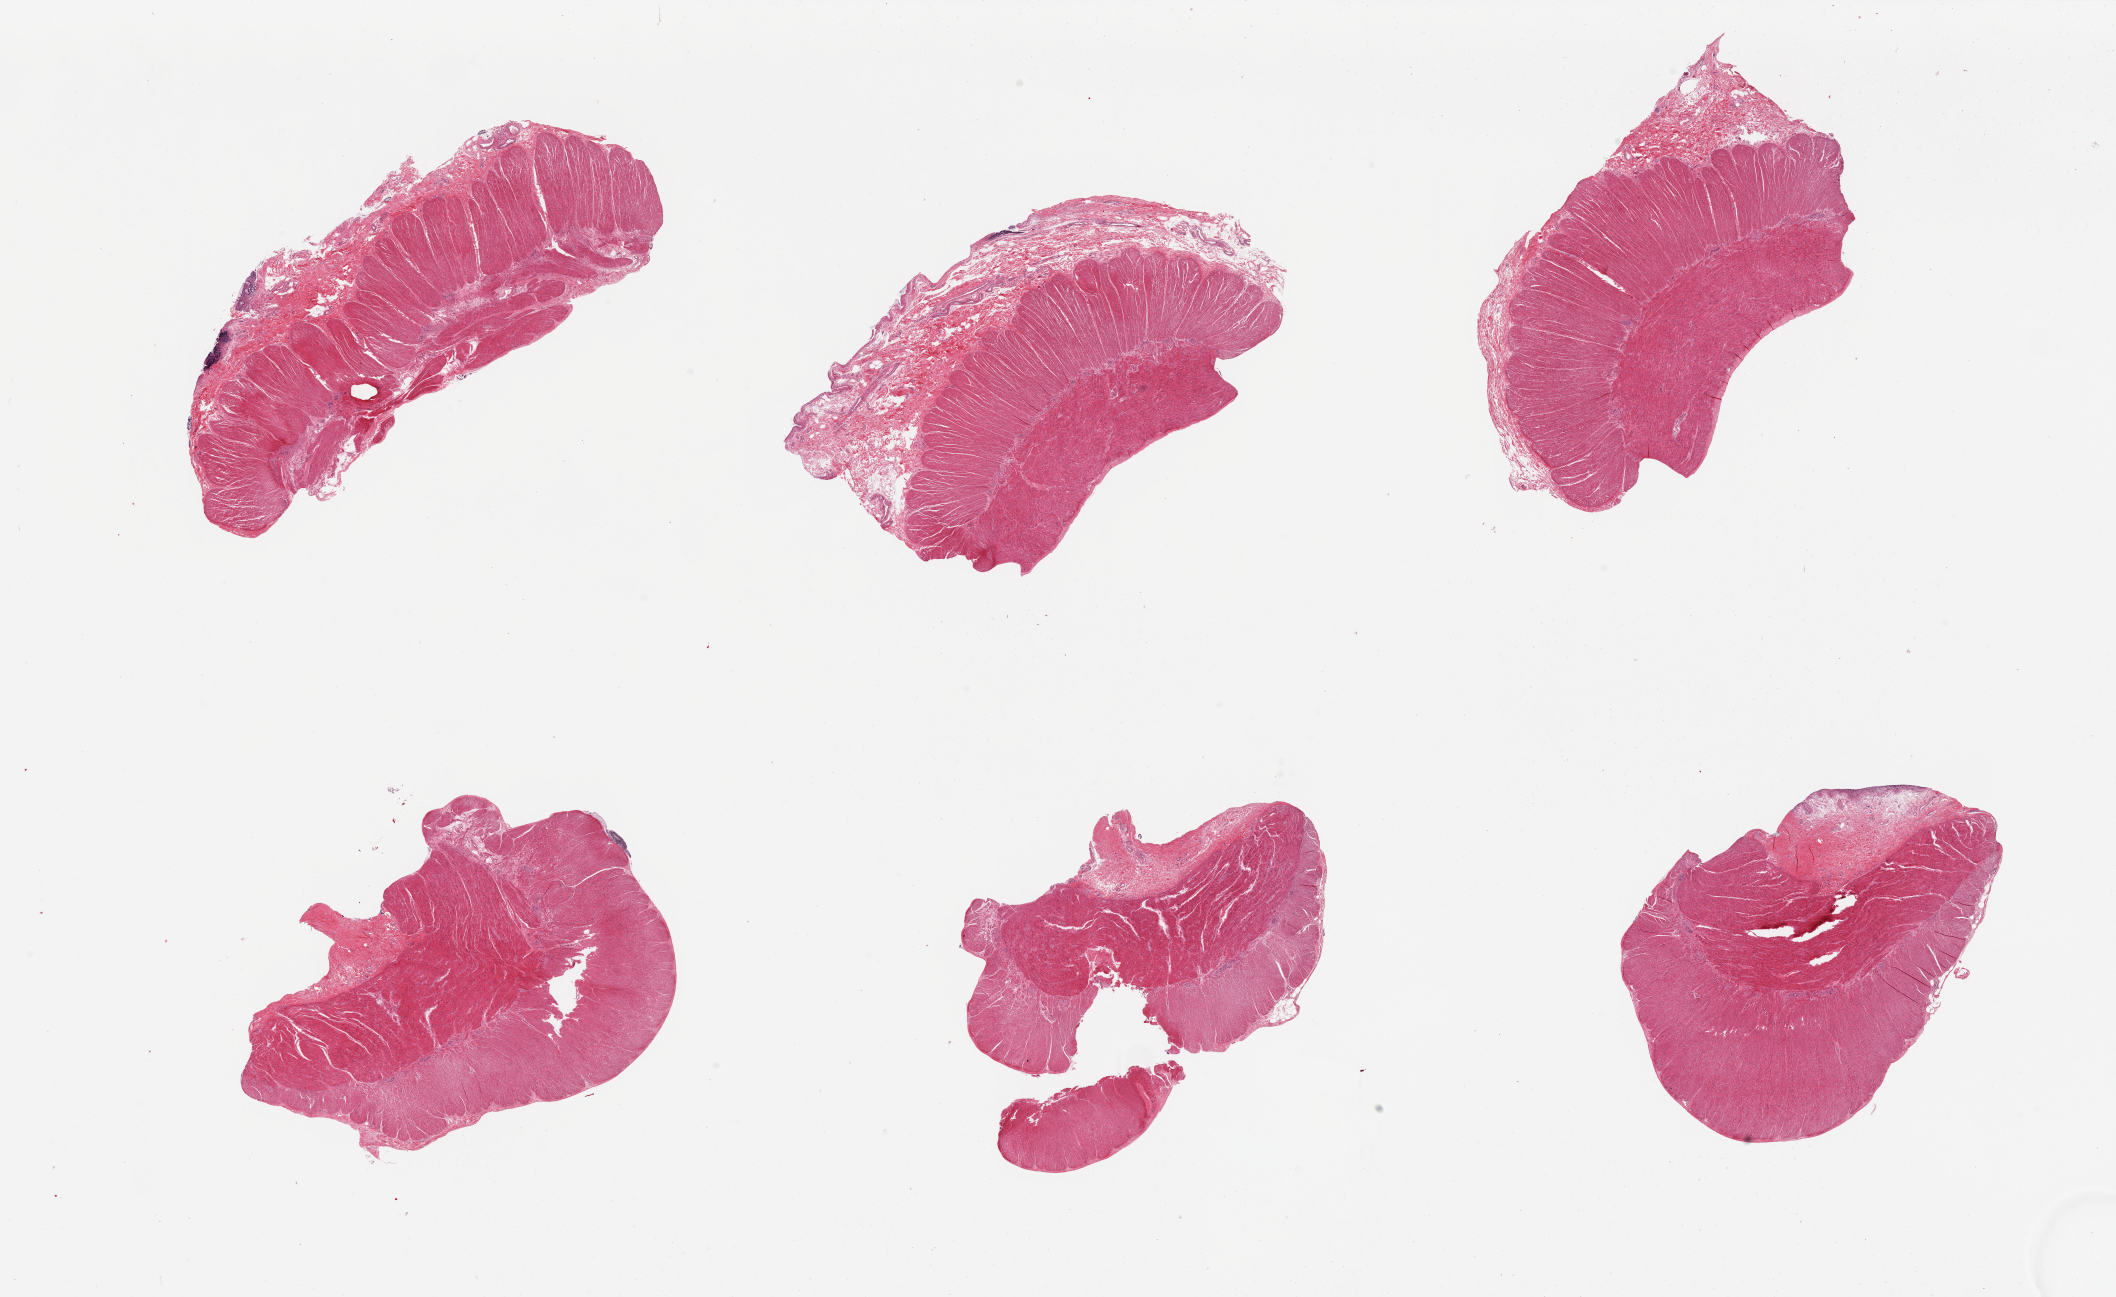
Hematoxylin and eosin (H&E) whole-slide image — a low-resolution overview of the entire scanned area, about 33.5 x 20.5 mm (acquisition: 20x scan), PAXgene-fixed, paraffin-embedded tissue, target tissue: sigmoid colon, tissue donor sample. Donor sex: female.
Review note (as recorded): 6 pieces, essentially all muscularis; minute focus of mucosa, good specimens.